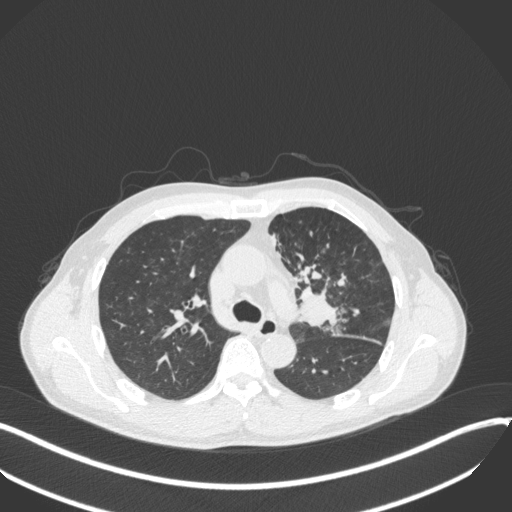
Chest CT, one axial slice; slice 227 of 411 in the series (ordered by position); 120 kVp; lung window (W 1500 / L -600 HU); 1 mm slice thickness; 512 × 512 image matrix. Male patient, age 56 years. From the clinical record (not read from this slice): clinical TNM (as recorded): T2a N0 M0.
Annotated regions visible in this slice (rectangle marked by the reading radiologist):
- lung tumour (recorded histology: squamous cell carcinoma): bounding box <294,282,343,336> (left, top, right, bottom; pixels)